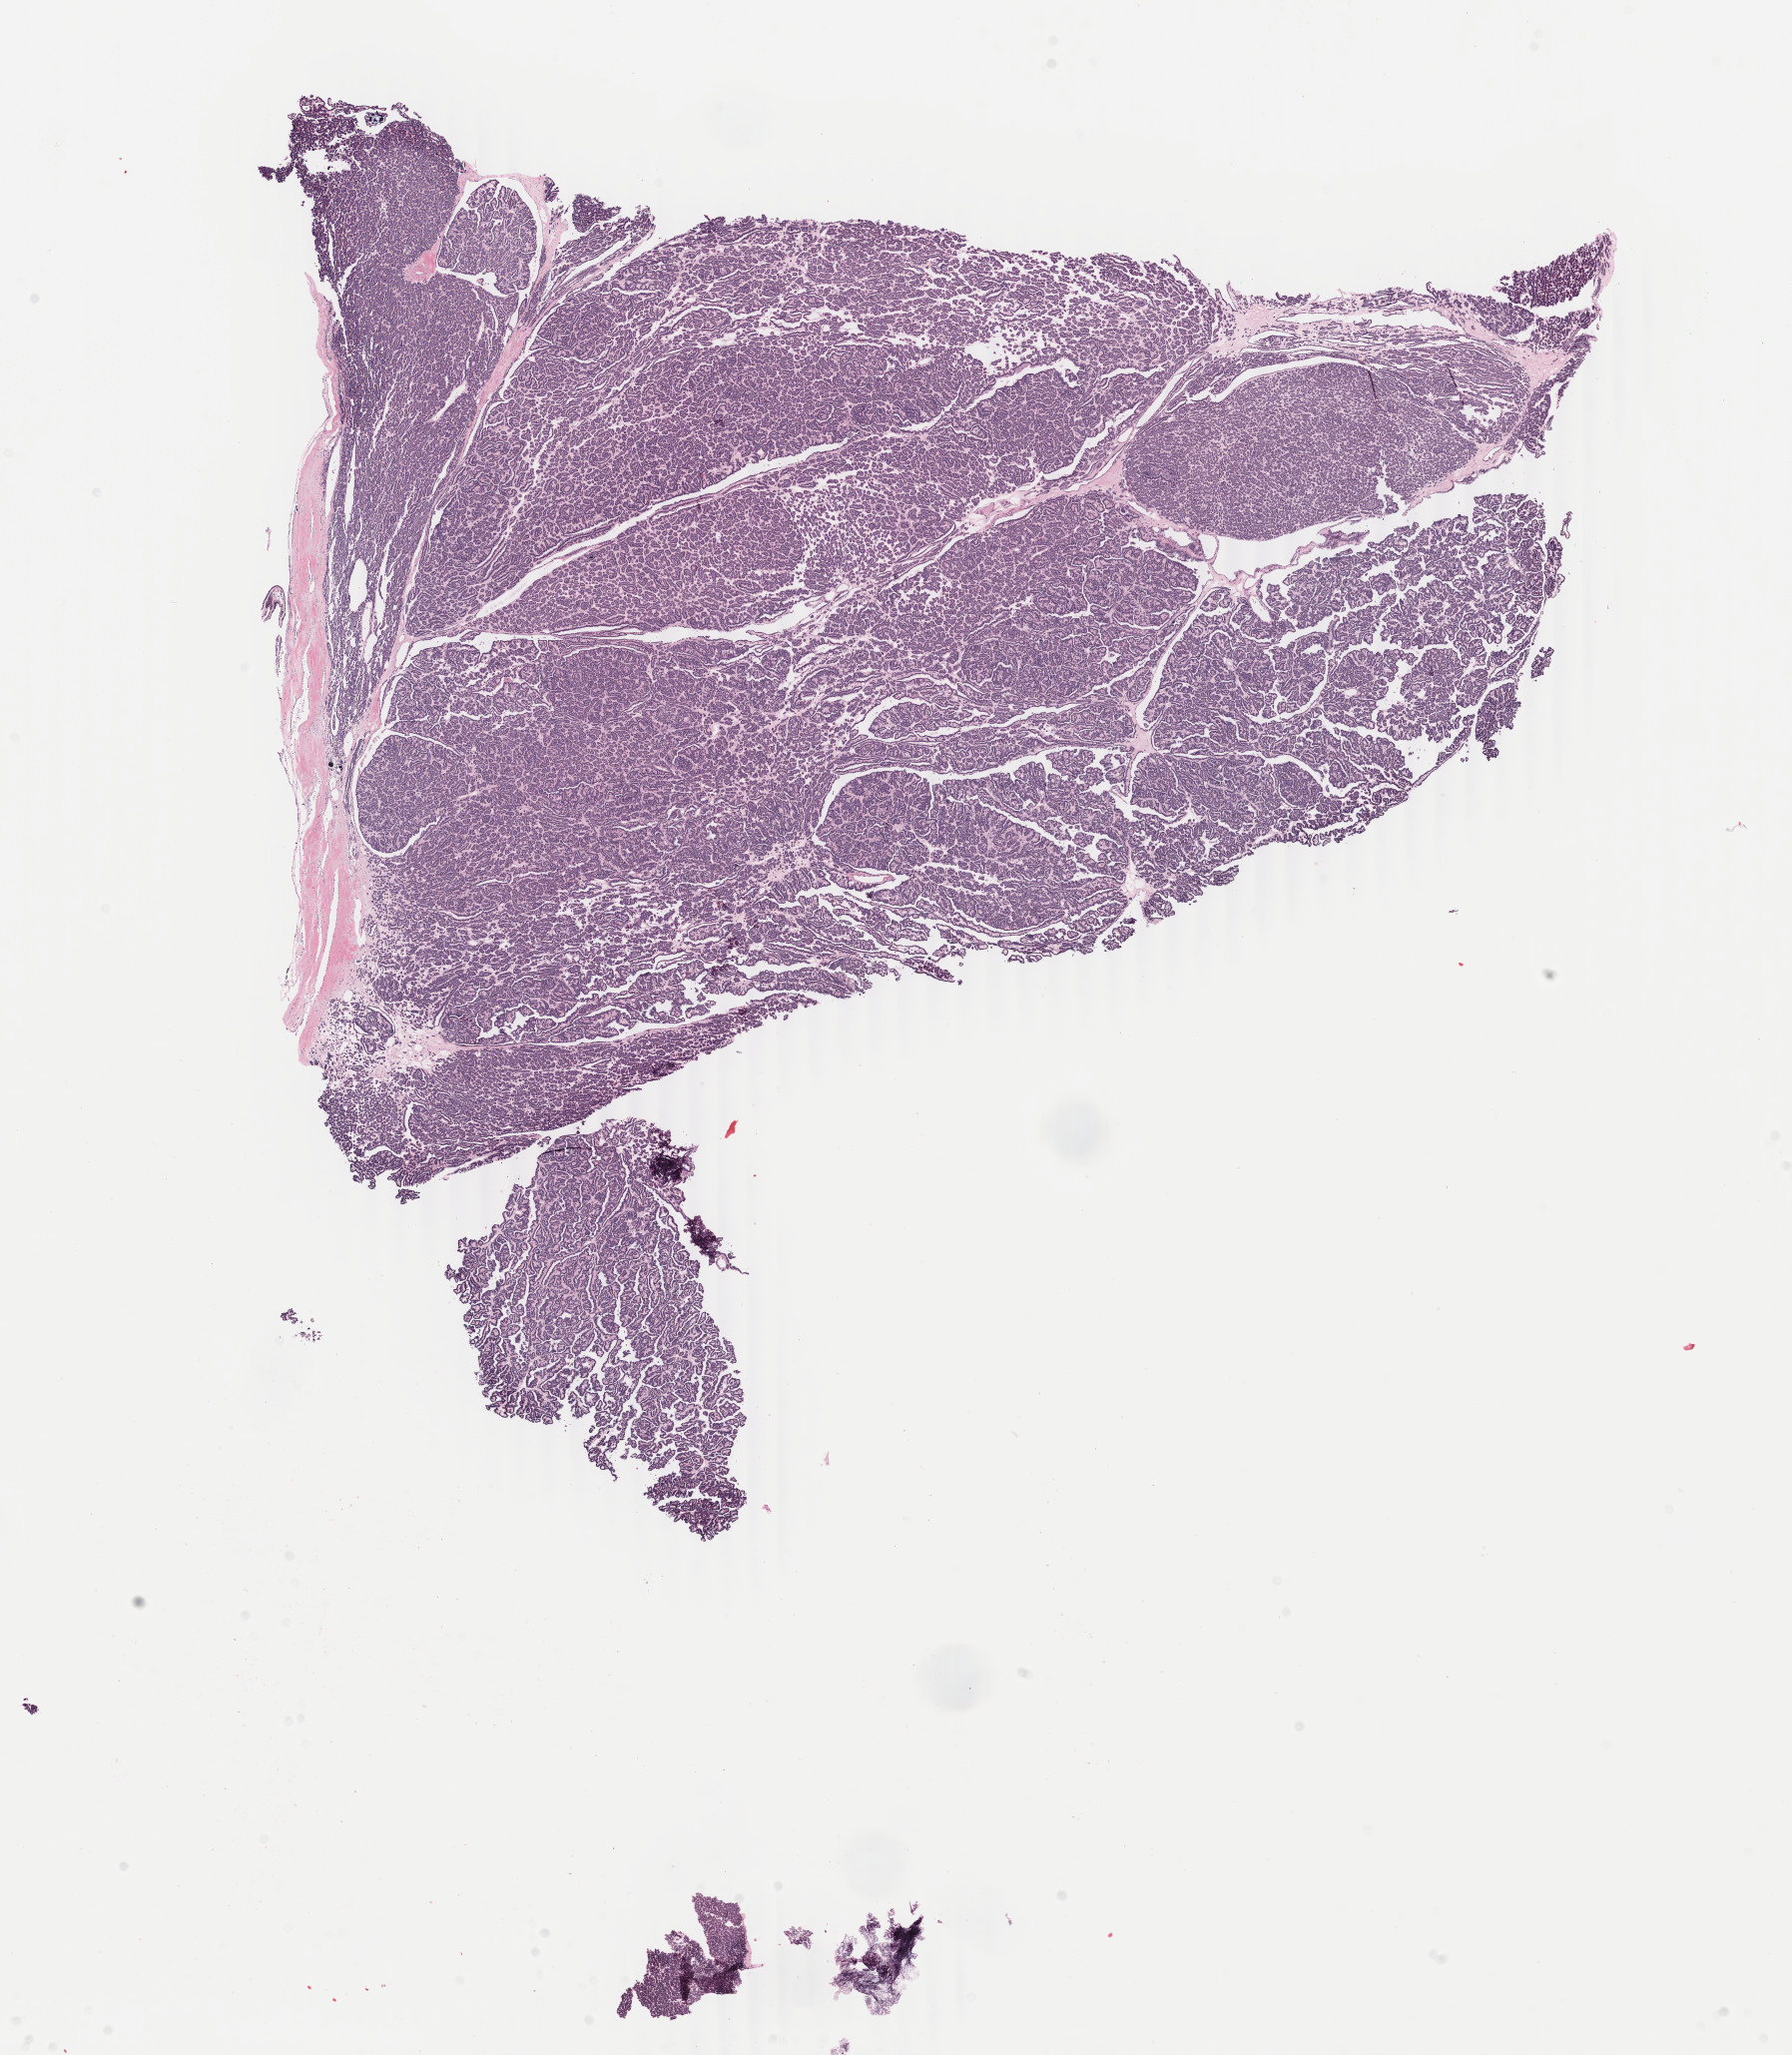
Digitized H&E tissue section (whole slide), a low-resolution overview of the entire scanned area, about 14.3 x 16.4 mm (from a 40x scan), formalin-fixed paraffin-embedded (FFPE) diagnostic section, sample: primary tumour, kidney. Female, age 54 years at initial diagnosis.
* histologic diagnosis: Papillary adenocarcinoma, NOS